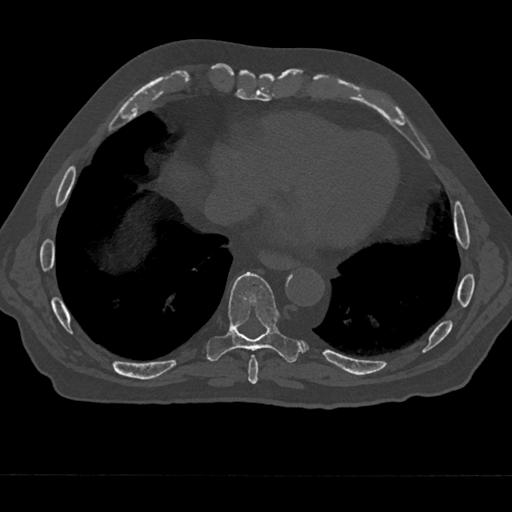
CT including the spine, one axial slice; slice 268 of 797 in the series (ordered by position); reconstruction kernel Br40s/3; 120 kVp; bone window (W 1800 / L 400 HU); 0.5 mm slice thickness; 512 × 512 image matrix, field of view 377 × 377 mm. Patient: male, 75 years. From the clinical record (not read from this slice): primary cancer: renal.
Structures marked on this image (semi-automatically segmented with operator editing):
- T8 vertebra: bounding box (x1, y1, x2, y2) in pixels: (248, 354, 259, 384)
- T9 vertebra: (206, 272, 302, 363)